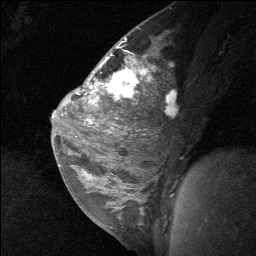
Breast MRI (dynamic contrast-enhanced), one sagittal slice; position 40 of 64 along the scan axis; dynamic contrast-enhanced study with each time point stored as its own series, time point 2 of 3 at this slice position (early post-contrast, ordered by acquisition time); 1.5 T; TE 4.8 ms, TR 27 ms; 2 mm slice thickness; 256 × 256 image matrix, field of view 180 × 180 mm. Female patient, age 26 years. From the clinical record (not read from this slice): setting: breast cancer imaged before/during neoadjuvant chemotherapy; receptor status: HR-positive, HER2-negative.
Structures marked on this image (semi-automatically segmented with operator editing):
- analysis volume of interest (the breast-tissue region the enhancement analysis was run in; not a lesion): bounding box [x1, y1, x2, y2] px = [86, 43, 156, 138]
- tumour enhancement mask (voxels above the 90 % enhancement threshold inside the analysis volume of interest): [89, 57, 146, 121]